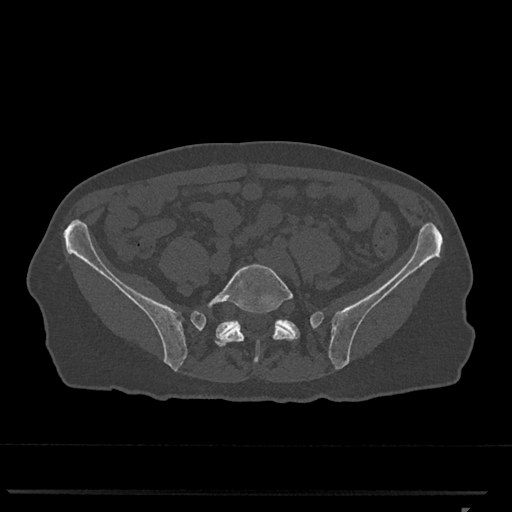
CT including the spine, one axial slice. Slice 137 of 793 in the series (ordered by position). 120 kVp. Bone window (W 1800 / L 400 HU). 0.5 mm slice thickness. 512 × 512 image matrix, field of view 380 × 380 mm. Patient: female, 62 years. From the clinical record (not read from this slice): primary cancer: renal.
Annotated regions visible in this slice (semi-automatic segmentation, software-assisted and operator-edited):
- L5 vertebra: bounding box (x1, y1, x2, y2) in pixels: (206, 264, 296, 363)